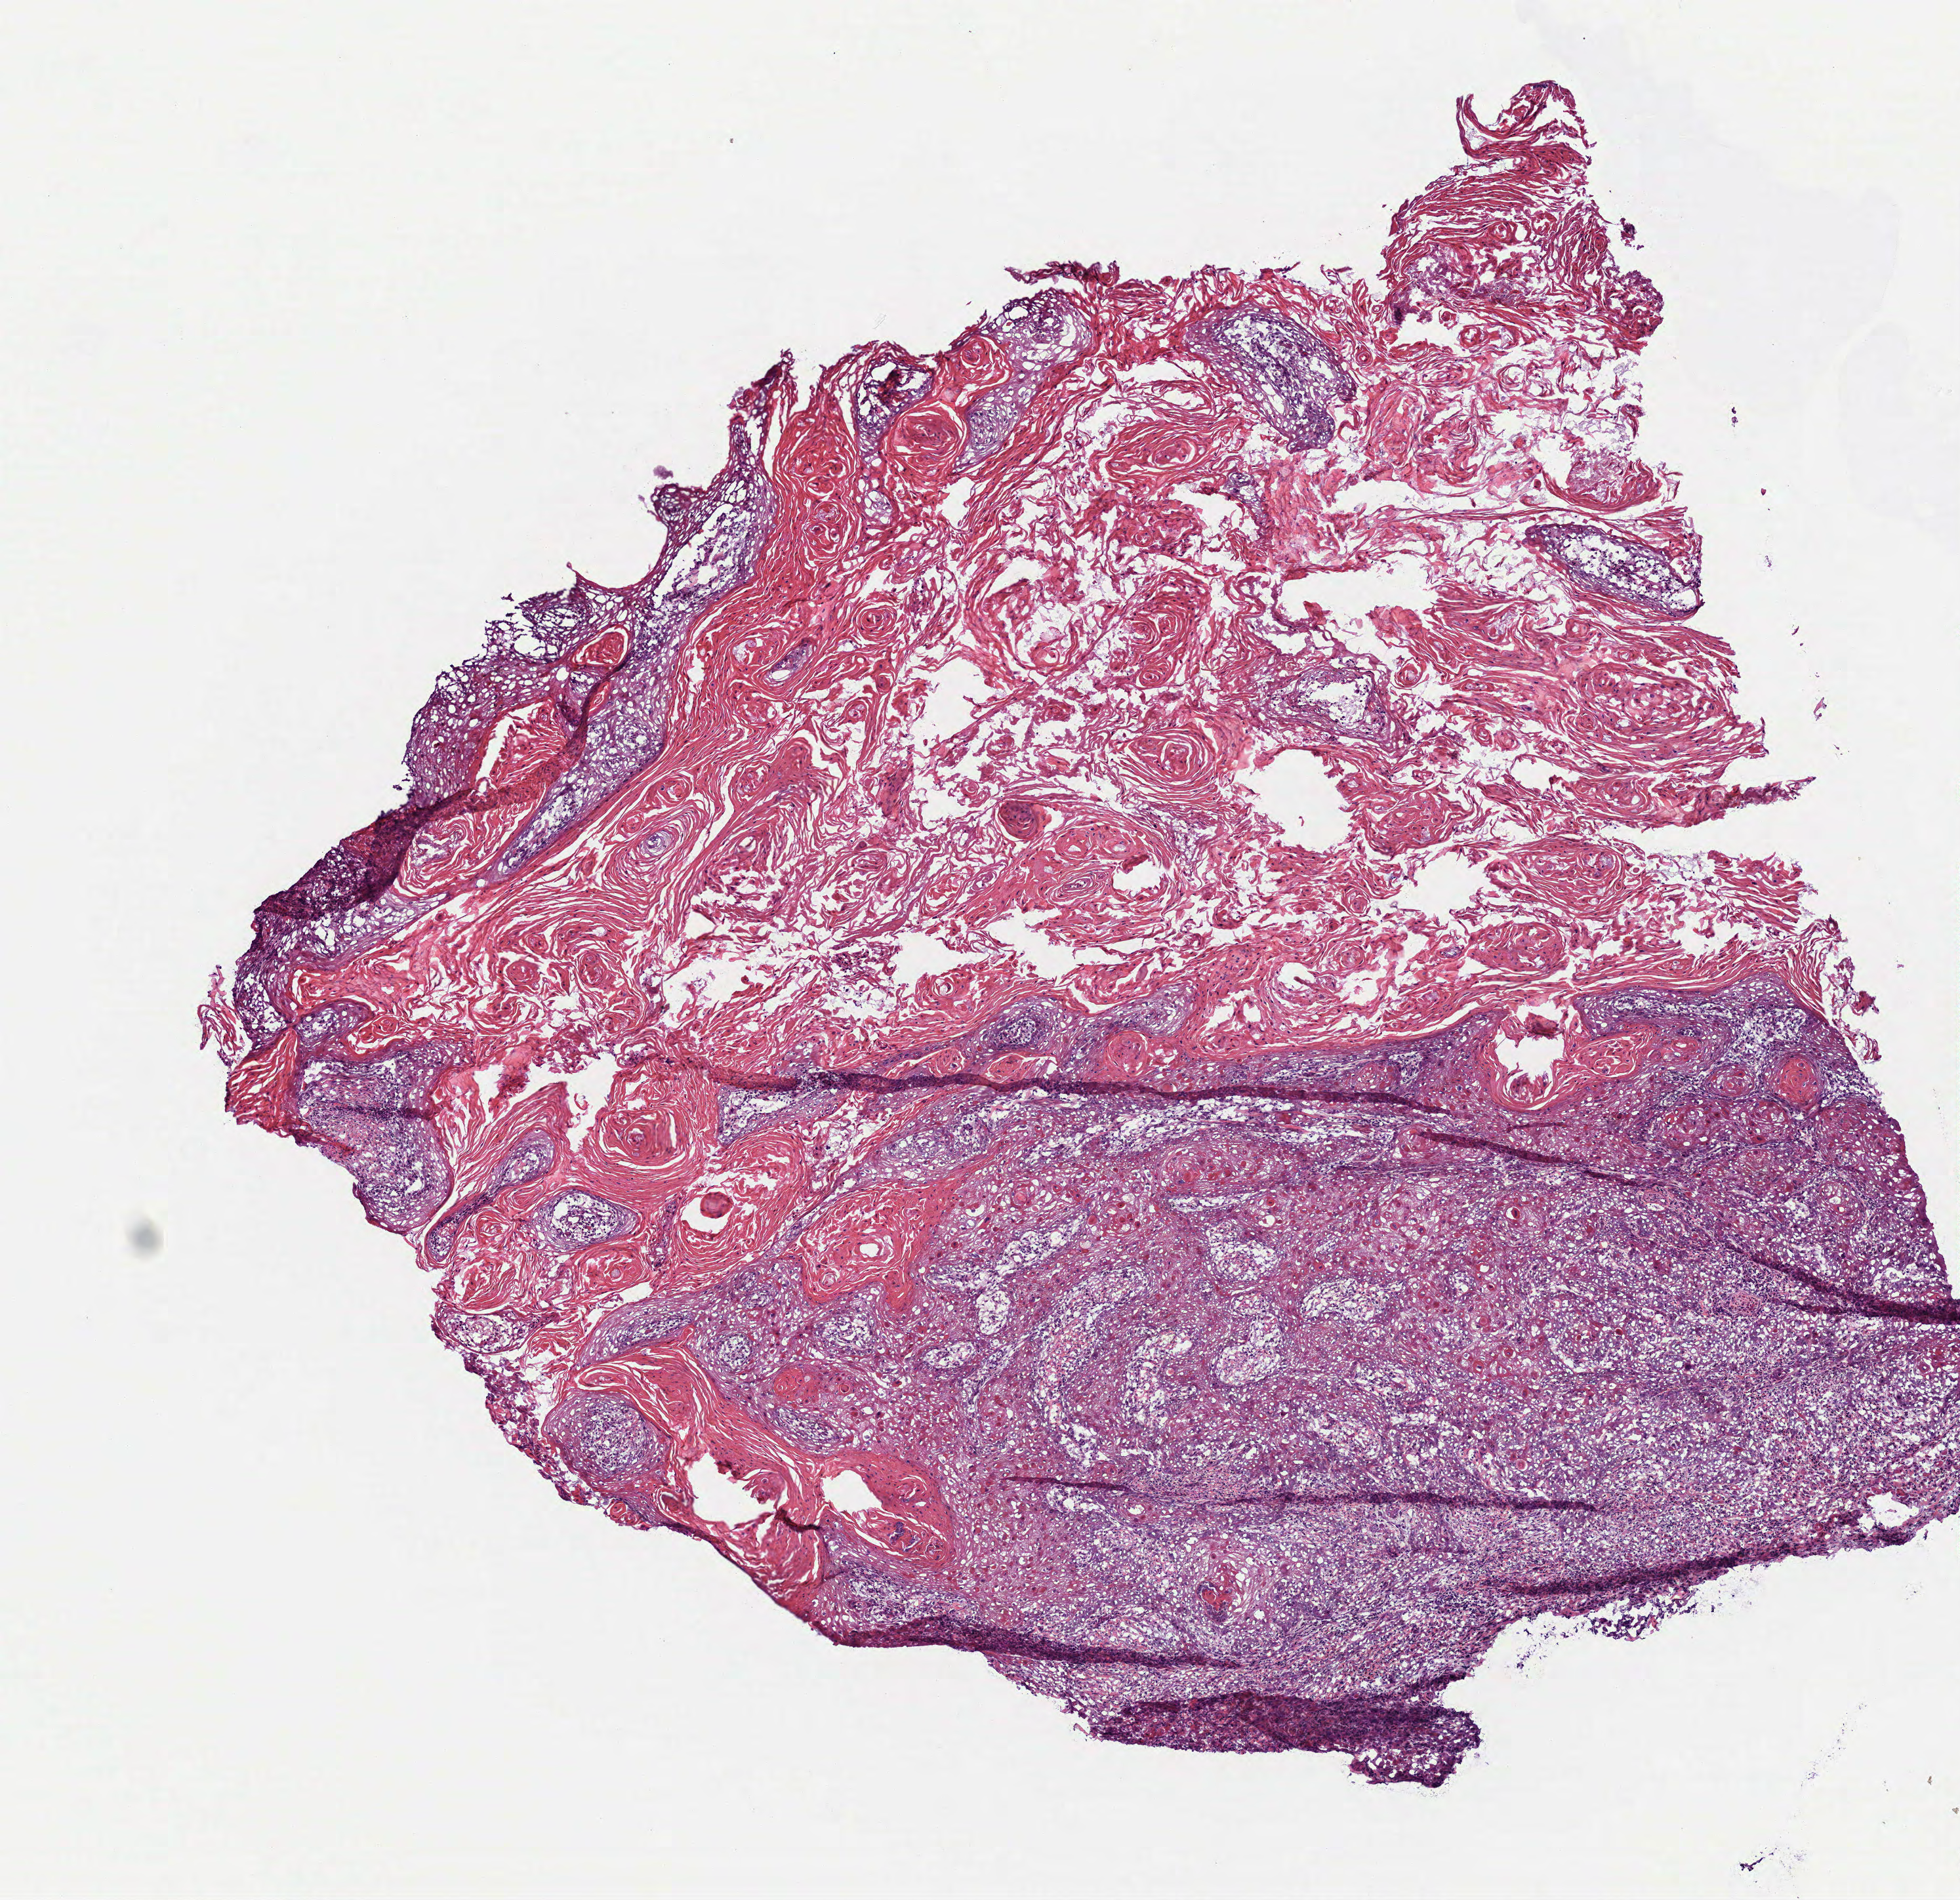
H&E-stained whole-slide image — low-resolution overview of the scanned area, about 6.0 x 5.8 mm. Frozen section from the top of the tissue portion. Sample: primary tumour, head and neck. Patient: male, age at initial diagnosis 61 years. Histologic grade: G2 (moderately differentiated). Pathologist review of this section (percent, as recorded): tumour cells 95%, tumour nuclei 90%, normal cells 0%, stromal cells 5%, necrosis 0%.
* diagnosis: Squamous cell carcinoma, NOS
* TNM: T2 N0
* AJCC pathologic stage: II (6th edition)